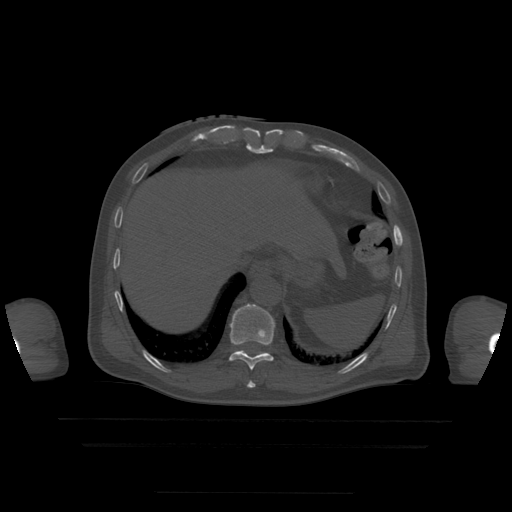
CT including the spine, one axial slice; bone window (W 1800 / L 400 HU); 1.25 mm slice thickness; 512 × 512 image matrix. Patient age 68 years. Case-level facts recorded for this patient, not image findings: primary cancer: urothelial.
Annotated regions visible in this slice (semi-automatically segmented with operator editing):
- T10 vertebra: bounding box [x1, y1, x2, y2] px = [229, 304, 276, 371]
- T9 vertebra: [247, 382, 256, 389]